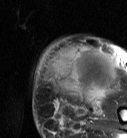
MRI of an extremity soft-tissue mass, one axial slice. Position 20 of 87 along the scan axis. T2-weighted fat-saturated. MR volume resampled by the dataset authors to the PET/CT grid (not the native acquisition matrix). 127 × 138 image matrix, field of view 124 × 135 mm. Female patient. Case-level facts recorded for this patient, not image findings: histological type: pleiomorphic leiomyosarcoma; grade: high; site of the primary tumour: left biceps.
Outlined on this slice (expert contour drawn on MRI and transferred to this co-registered scan by the dataset authors):
- gross tumour volume including surrounding oedema: bounding box (x1, y1, x2, y2) in pixels: (47, 46, 117, 104)
- gross tumour volume (mass): (47, 46, 115, 97)